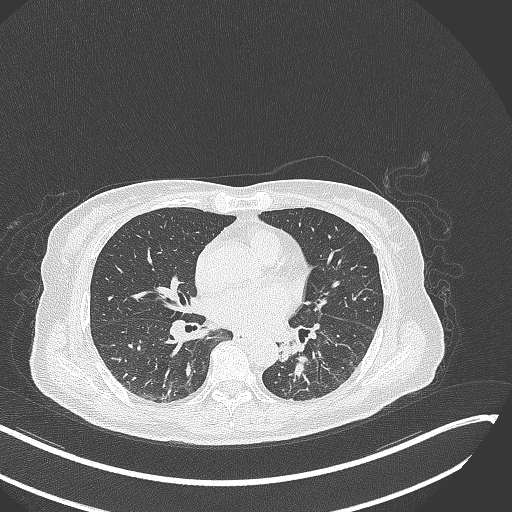
Chest CT, one axial slice; position 126 of 342 along the scan axis; 120 kVp; lung window (W 1500 / L -600 HU); 1 mm slice thickness; 512 × 512 image matrix. Patient: female, 64 years. Case-level facts recorded for this patient, not image findings: clinical TNM (as recorded): T3 N1 M1; histopathological grade: G3.
Annotated regions visible in this slice (bounding box drawn by a radiologist):
- lung tumour (recorded histology: small cell carcinoma): bounding box (x1, y1, x2, y2) in pixels: (276, 336, 310, 379)